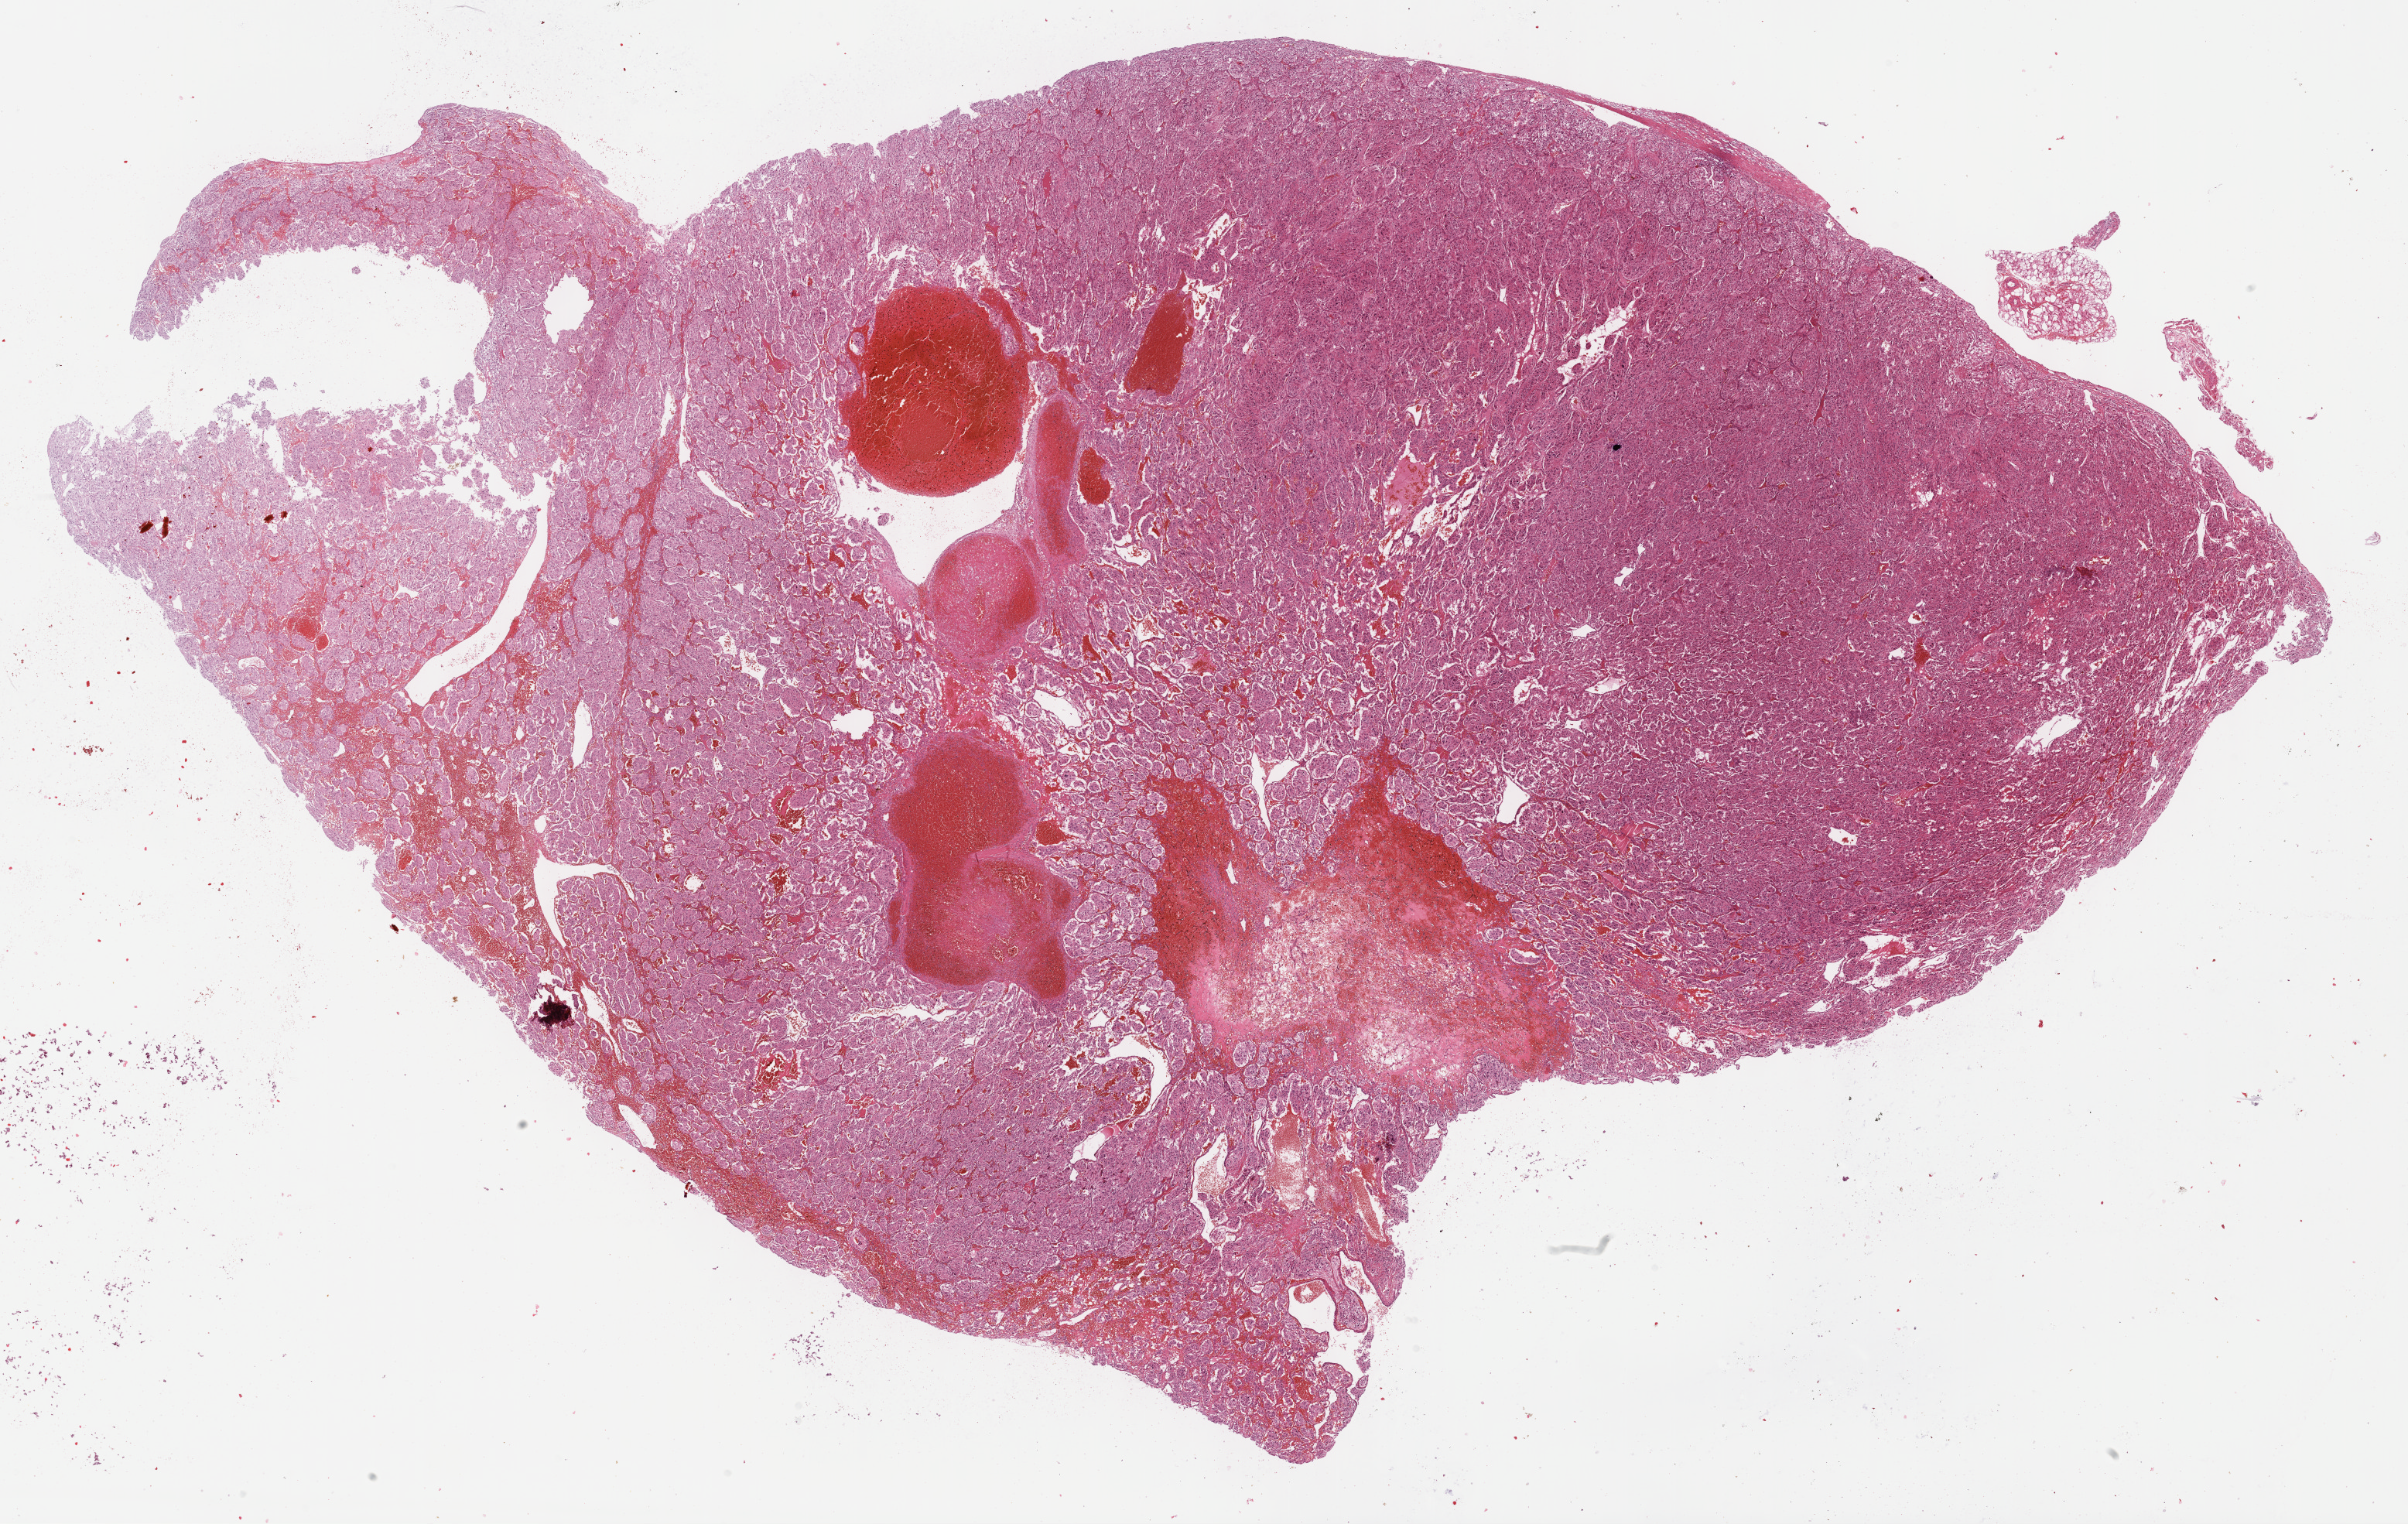
H&E-stained whole-slide image, whole scanned area (about 25.2 x 15.9 mm, slide scanned at 40x) shown as a low-resolution overview. FFPE section. Sample: primary tumour, adrenal gland. Female, age 25 years at initial diagnosis.
Diagnosis: Pheochromocytoma, NOS.